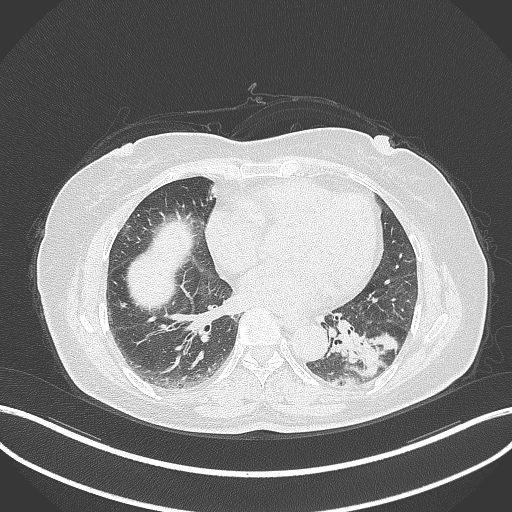
Chest CT, one axial slice; position 154 of 311 along the scan axis; reconstruction kernel B70f; 120 kVp; lung window (W 1500 / L -600 HU); 1 mm slice thickness; 512 × 512 image matrix. Female patient, age 59 years. Case-level facts recorded for this patient, not image findings: clinical TNM (as recorded): T2a N0 M0; histopathological grade: G2-3.
Annotated regions visible in this slice (rectangle marked by the reading radiologist):
- lung tumour (recorded histology: adenocarcinoma): bounding box (x1, y1, x2, y2) in pixels: (347, 323, 401, 378)